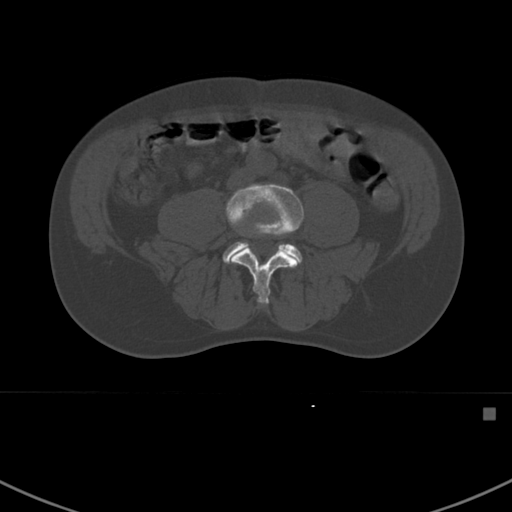
CT including the spine, one axial slice; slice 234 of 412 in the series (ordered by position); 120 kVp; bone window (W 1800 / L 400 HU); 1.5 mm slice thickness; 512 × 512 image matrix, field of view 358 × 358 mm. Male patient, age 59 years. From the clinical record (not read from this slice): primary cancer: prostate.
Structures marked on this image (semi-automatic segmentation, software-assisted and operator-edited):
- L4 vertebra: bounding box [x1, y1, x2, y2] px = [225, 184, 304, 305]
- L5 vertebra: [223, 242, 302, 264]